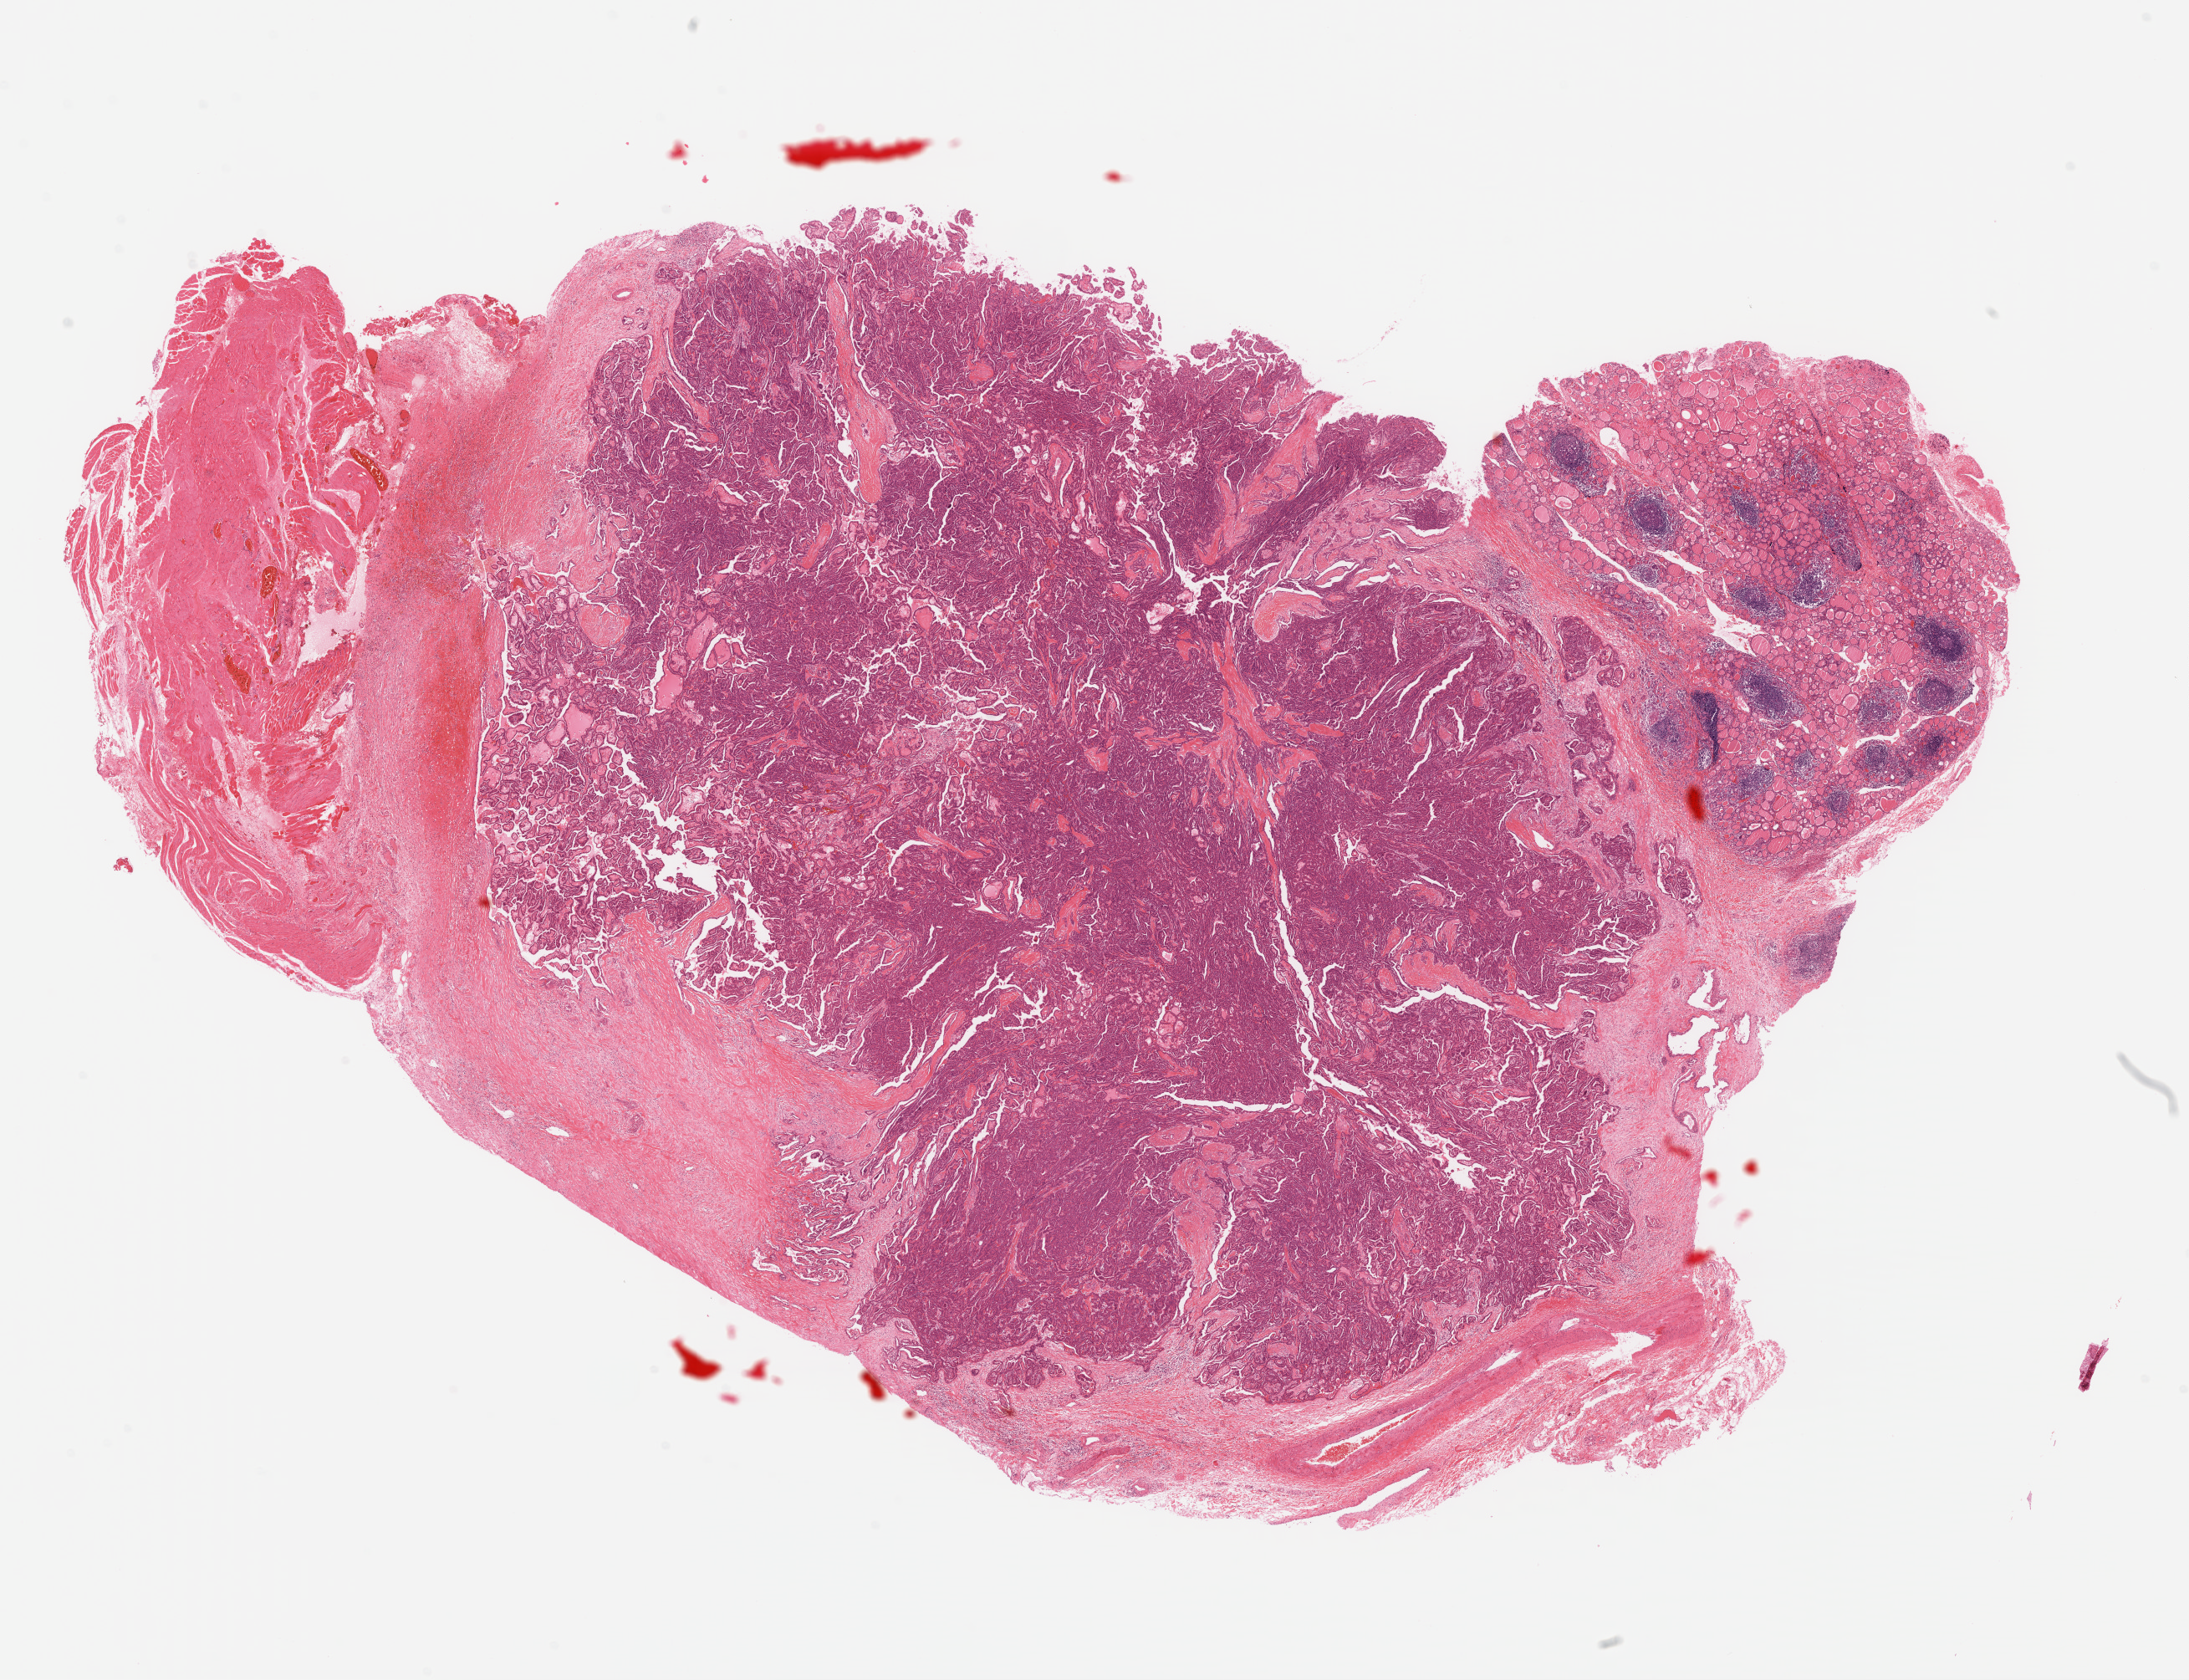
Digitized H&E-stained tissue section (whole slide), whole scanned area (about 20.6 x 15.8 mm) shown as a low-resolution overview. Formalin-fixed paraffin-embedded (FFPE) diagnostic section. Thyroid, primary tumour sample. Female patient; age at initial diagnosis 50 years.
TNM: T1b N0 M0. AJCC pathologic stage: I (7th edition). Lymph nodes positive (case pathology): 0 of 3 examined. Histologic diagnosis: Papillary adenocarcinoma, NOS (thyroid gland).